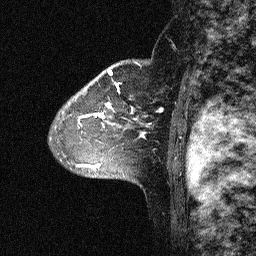
Breast MRI (dynamic contrast-enhanced), one sagittal slice; slice 46 of 64 in the series (ordered by position); dynamic contrast-enhanced study with each time point stored as its own series, time point 2 of 3 at this slice position (early post-contrast, ordered by acquisition time); 1.5 T; TE 4.5 ms, TR 11 ms; 2.06 mm slice thickness; 256 × 256 image matrix, field of view 200 × 200 mm. Patient: female, 46 years. From the clinical record (not read from this slice): setting: breast cancer imaged before/during neoadjuvant chemotherapy; receptor status: HER2-positive.
Annotated regions visible in this slice (semi-automatic segmentation, software-assisted and operator-edited):
- analysis volume of interest (the breast-tissue region the enhancement analysis was run in; not a lesion): bounding box [x1, y1, x2, y2] px = [43, 72, 164, 177]
- tumour enhancement mask (voxels above the 90 % enhancement threshold inside the analysis volume of interest): [77, 72, 163, 167]